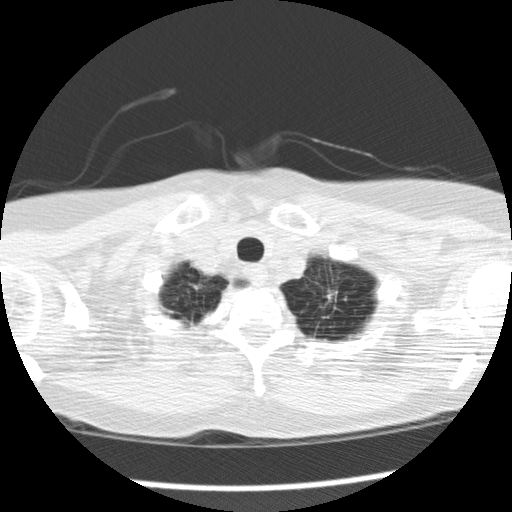
Chest CT (low-dose screening protocol), one axial image; second annual screen; lung window (W 1500 / L -600 HU); 2.5 mm slice thickness; standard (soft-tissue) reconstruction kernel (STANDARD); slice 148 of 159 in the series. Female, age 69 years at enrolment.
Expert-annotated lung lesion, bounding box [x1, y1, x2, y2] px = [311, 274, 368, 324]. The screening reader recorded 2 non-calcified nodules or masses ≥4 mm on this exam (right upper lobe, lingula); which of them this box marks is not recorded. Official screen result: positive, change unspecified: nodule(s) >= 4 mm or enlarging nodule(s), mass(es), or other non-specific abnormalities suspicious for lung cancer. Later outcome: lung cancer diagnosed 147 days after this screen — adenocarcinoma, NOS, left upper lobe, poorly differentiated (G3), stage IB (AJCC 6th edition), 80 mm at pathology.